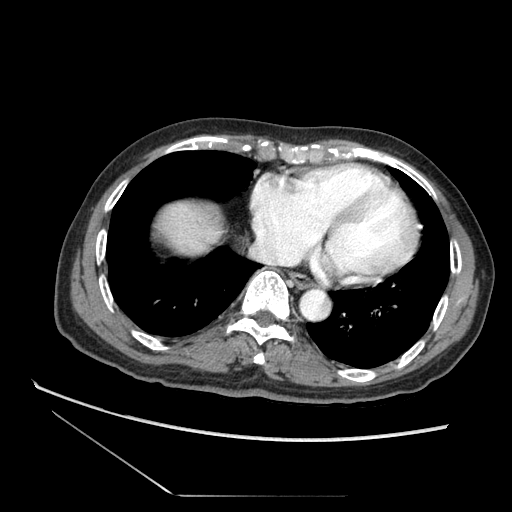
Contrast-enhanced abdominal CT (liver protocol), one axial slice. Slice 73 of 73 in the series (ordered by position). Reconstruction kernel STANDARD. 120 kVp. Soft-tissue window (W 400 / L 40 HU). 512 × 512 image matrix, field of view 360 × 360 mm. From the clinical record (not read from this slice): diagnosis: hepatocellular carcinoma (patient treated with transarterial chemoembolisation; whether this scan precedes or follows treatment is not stated here); TNM stage (as recorded): Stage-II; Child-Pugh class: A; tumour nodularity: multinodular.
Outlined on this slice (semi-automatic segmentation, software-assisted and operator-edited):
- liver parenchyma outside the tumour (the mass and vessels are separate outlines, so this box may not span the whole liver): bounding box <148,188,234,272> (left, top, right, bottom; pixels)
- liver vessels: <181,200,184,203>